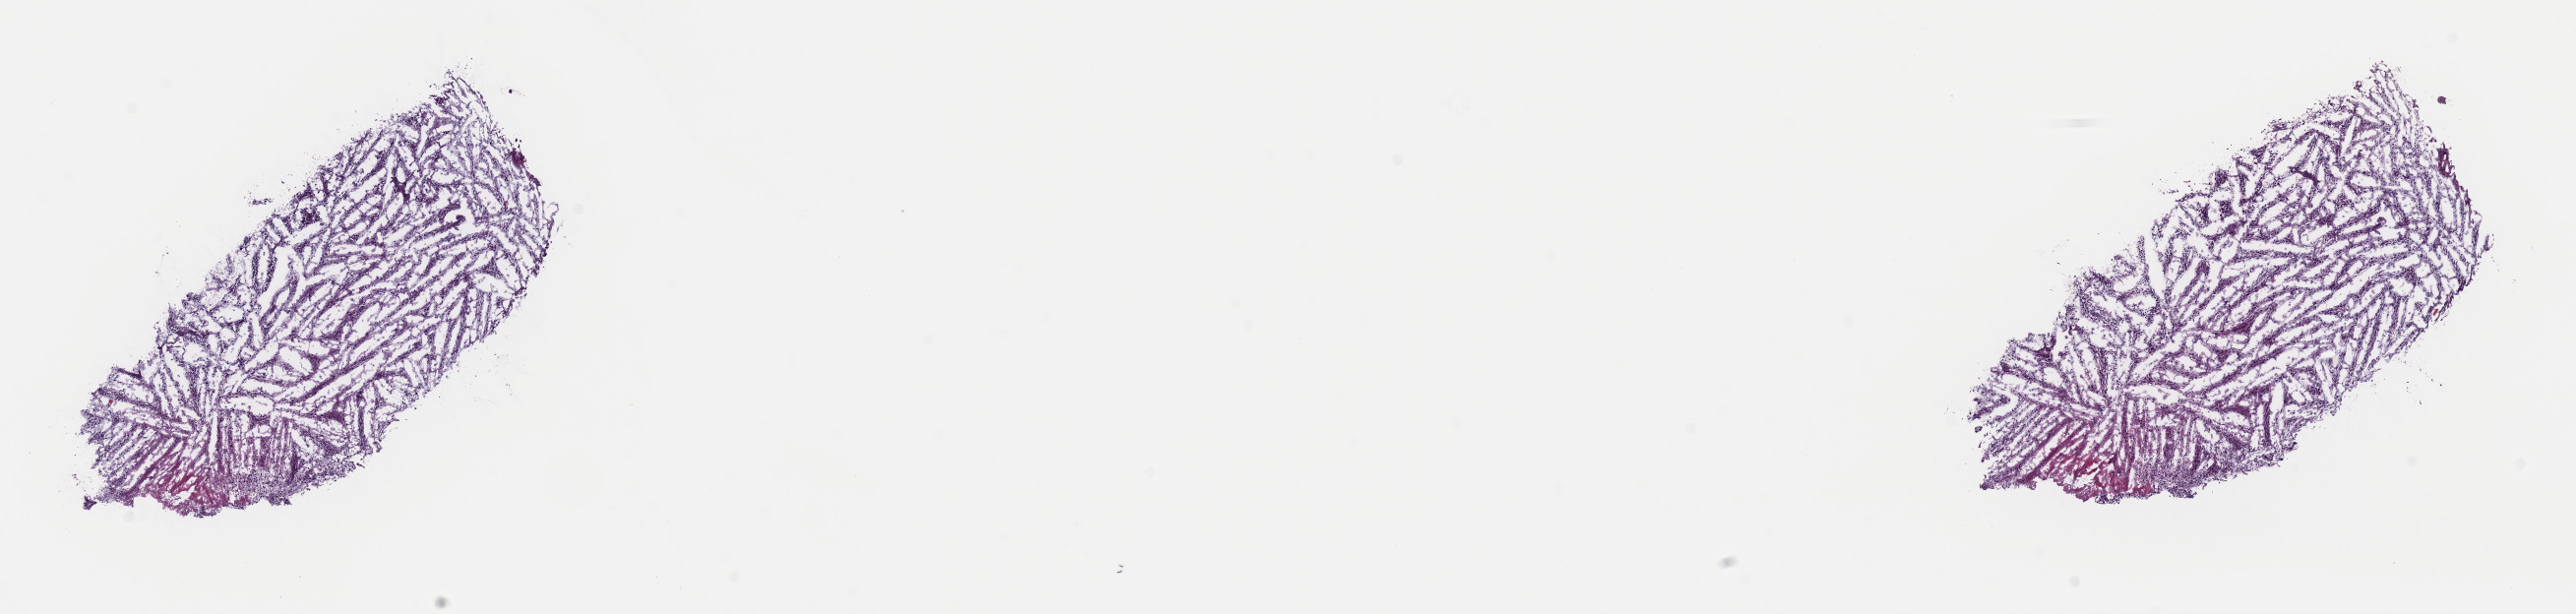
Whole-slide histology image, H&E-stained, low-resolution overview of the scanned area, about 20.7 x 4.9 mm (from a 40x scan); frozen section from the top of the tissue portion; sample: primary tumour, brain. Patient: male, age at initial diagnosis 51 years. Histologic grade: G3 (poorly differentiated). Slide review estimates, as recorded: tumour cells 80%, tumour nuclei 90%, normal cells 5%, stromal cells 15%, necrosis 0%. Infiltration values recorded for this section: lymphocyte infiltration 0%, monocyte infiltration 0%, neutrophil infiltration 0%.
Diagnosis: Mixed glioma (cerebrum). Laterality: right.